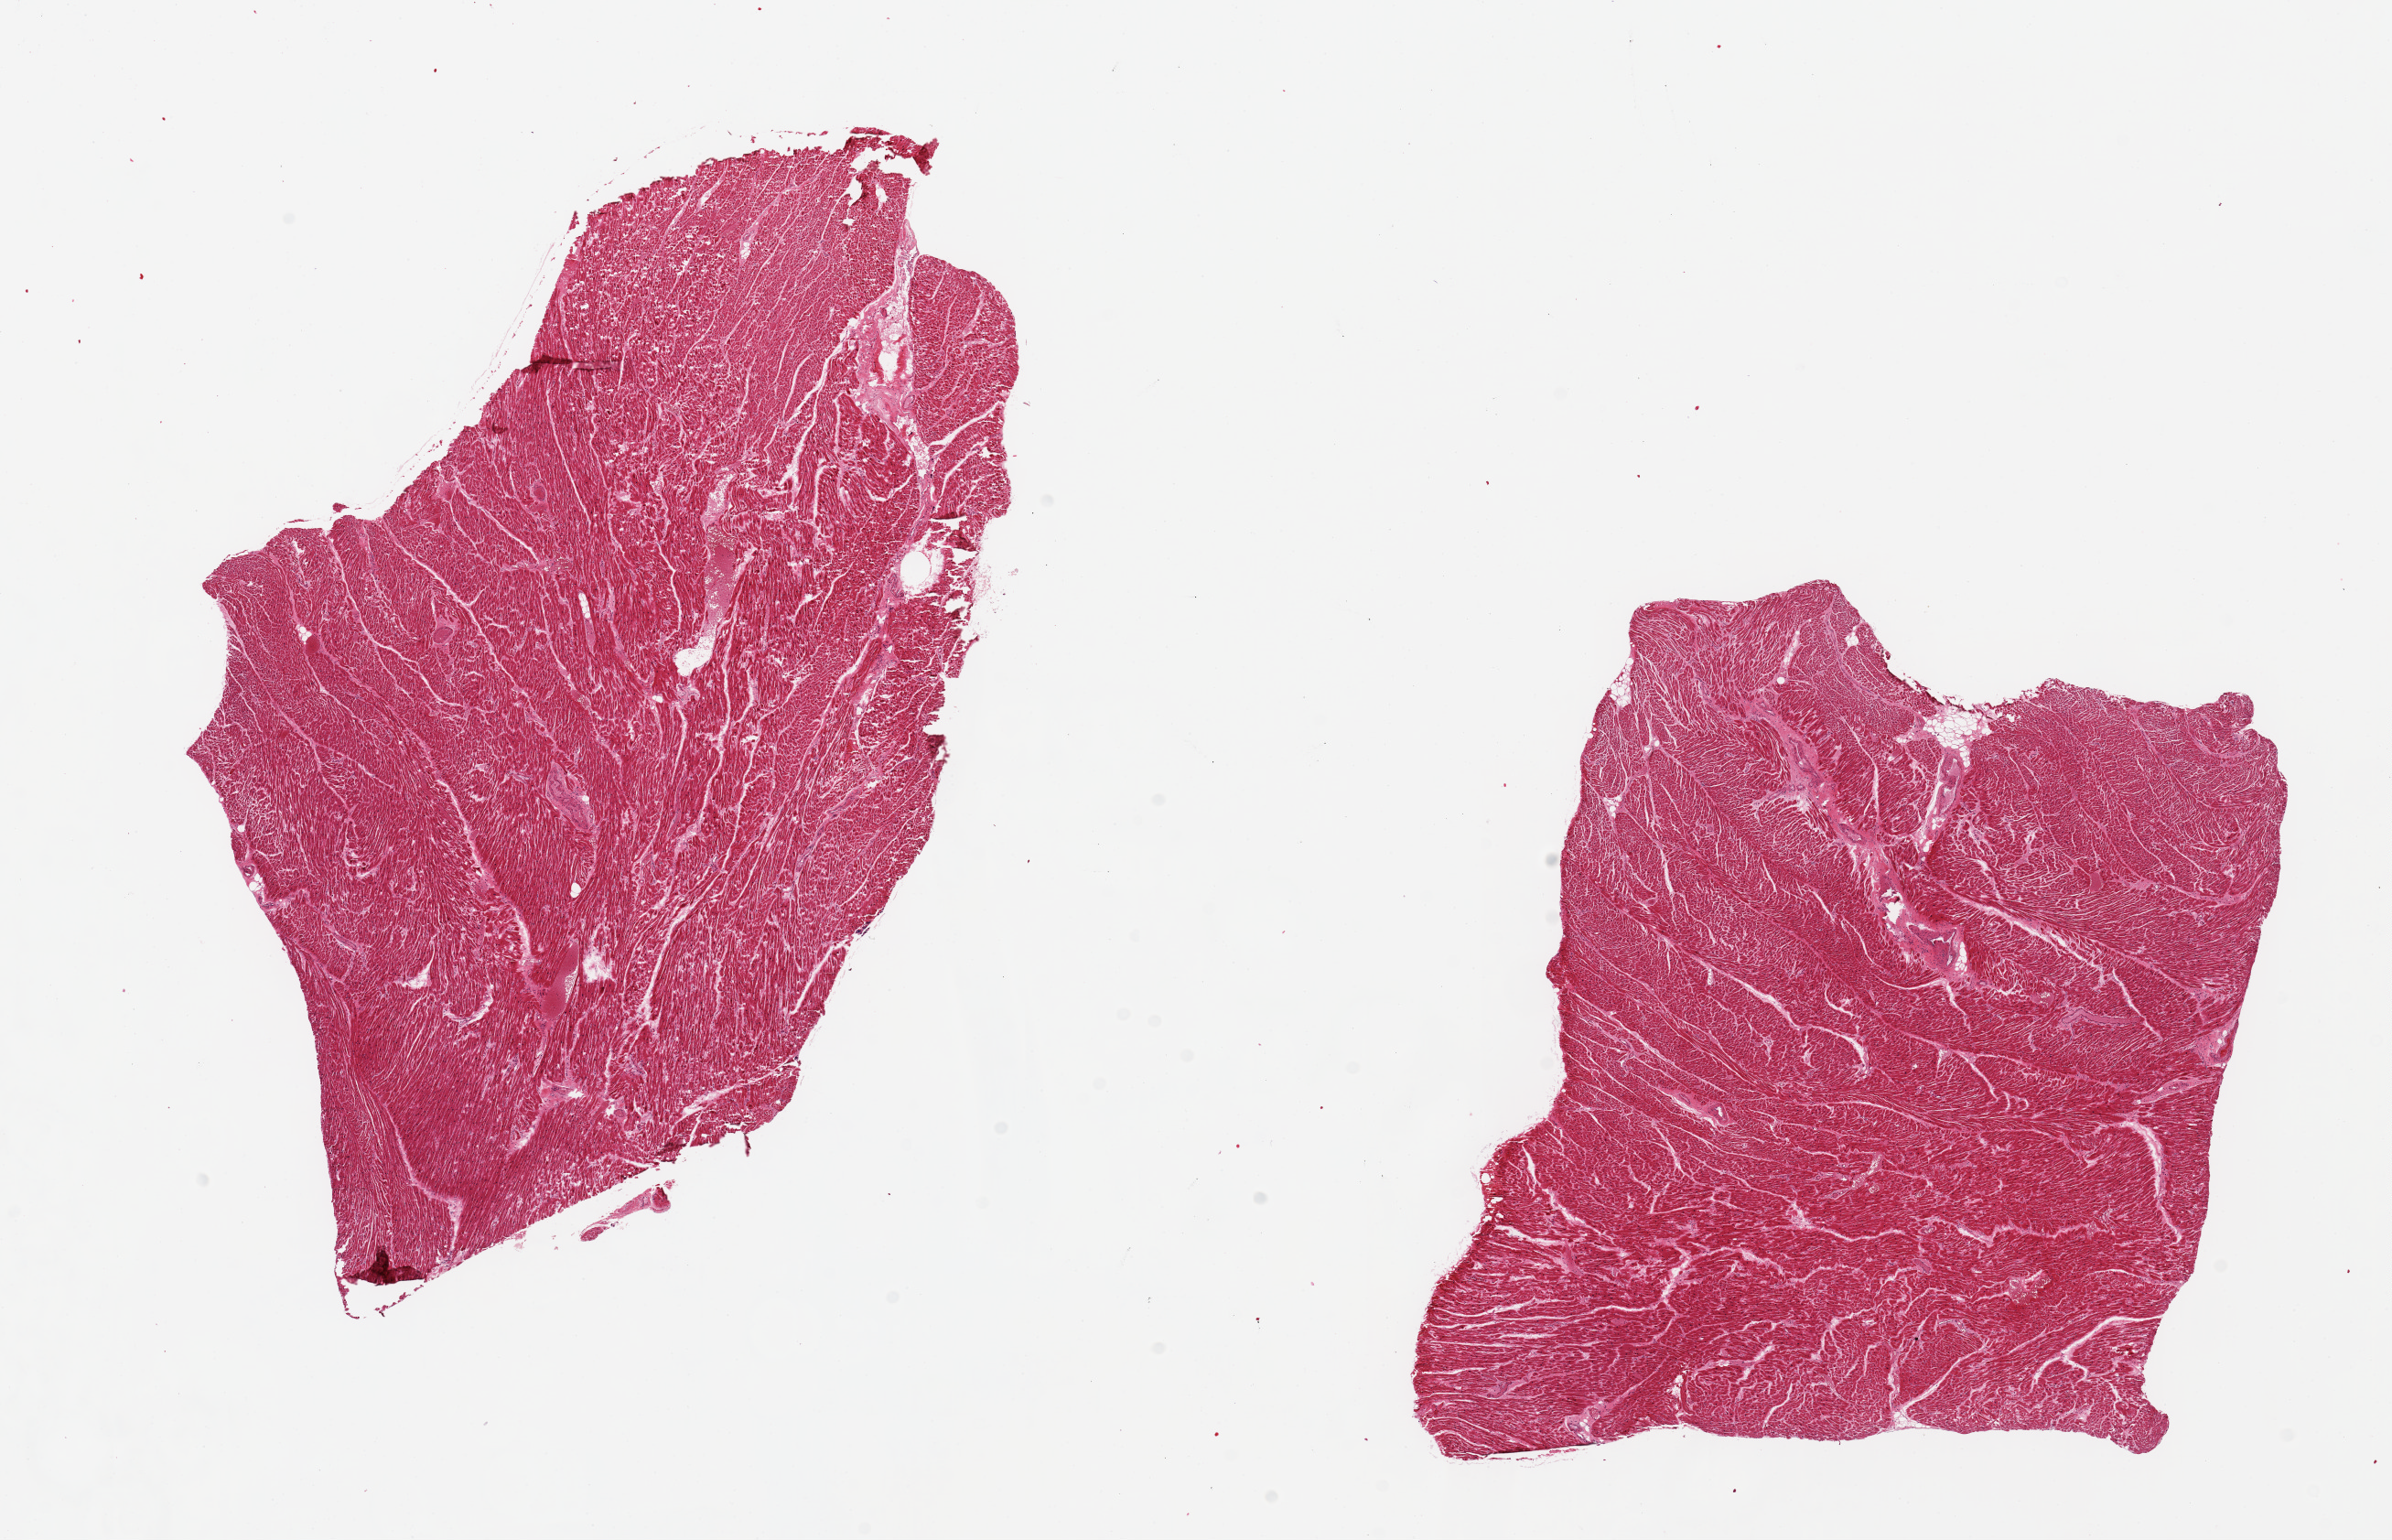
Haematoxylin and eosin whole-slide image, shown as a low-resolution overview of the whole scanned area (about 20.7 x 13.3 mm); PAXgene-fixed paraffin-embedded (PFPE) section; section of heart (target tissue); tissue donor sample. Donor: male.
- review note (as recorded): 2 pieces, 11x7 & 8x6.5mm; Hypertrophic fibers